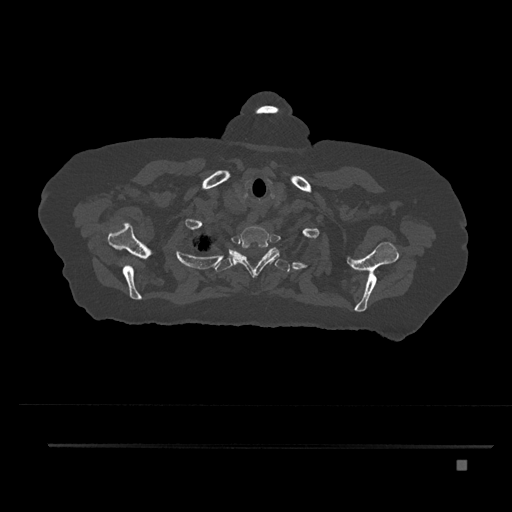
CT including the spine, one axial slice. Position 688 of 797 along the scan axis. 120 kVp. Bone window (W 1800 / L 400 HU). 0.5 mm slice thickness. 512 × 512 image matrix, field of view 437 × 437 mm. Female patient, age 76 years. Case-level facts recorded for this patient, not image findings: primary cancer: lung.
Outlined on this slice (semi-automatically segmented with operator editing):
- T1 vertebra: bounding box (x1, y1, x2, y2) in pixels: (229, 225, 279, 278)
- T2 vertebra: (207, 248, 290, 272)